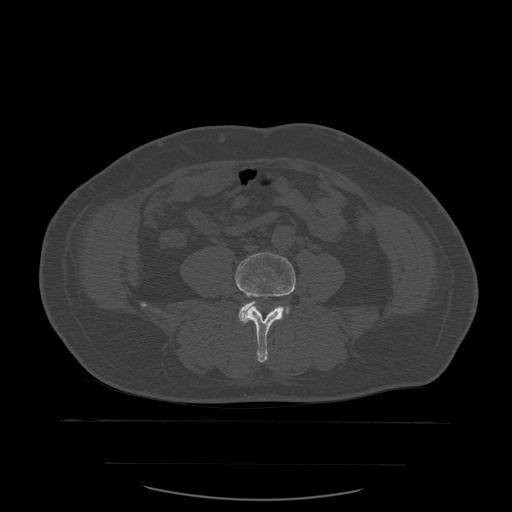
CT including the spine, one axial slice. Slice 159 of 590 in the series (ordered by position). Bone window (W 1800 / L 400 HU). 1.25 mm slice thickness. 512 × 512 image matrix. Patient age 71 years. Case-level facts recorded for this patient, not image findings: primary cancer: lung; vertebrae with lytic lesions (as recorded): T1, T2, L5, S1.
Annotated regions visible in this slice (semi-automatically segmented with operator editing):
- L4 vertebra: bounding box <235,253,296,363> (left, top, right, bottom; pixels)
- L5 vertebra: <239,296,283,322>